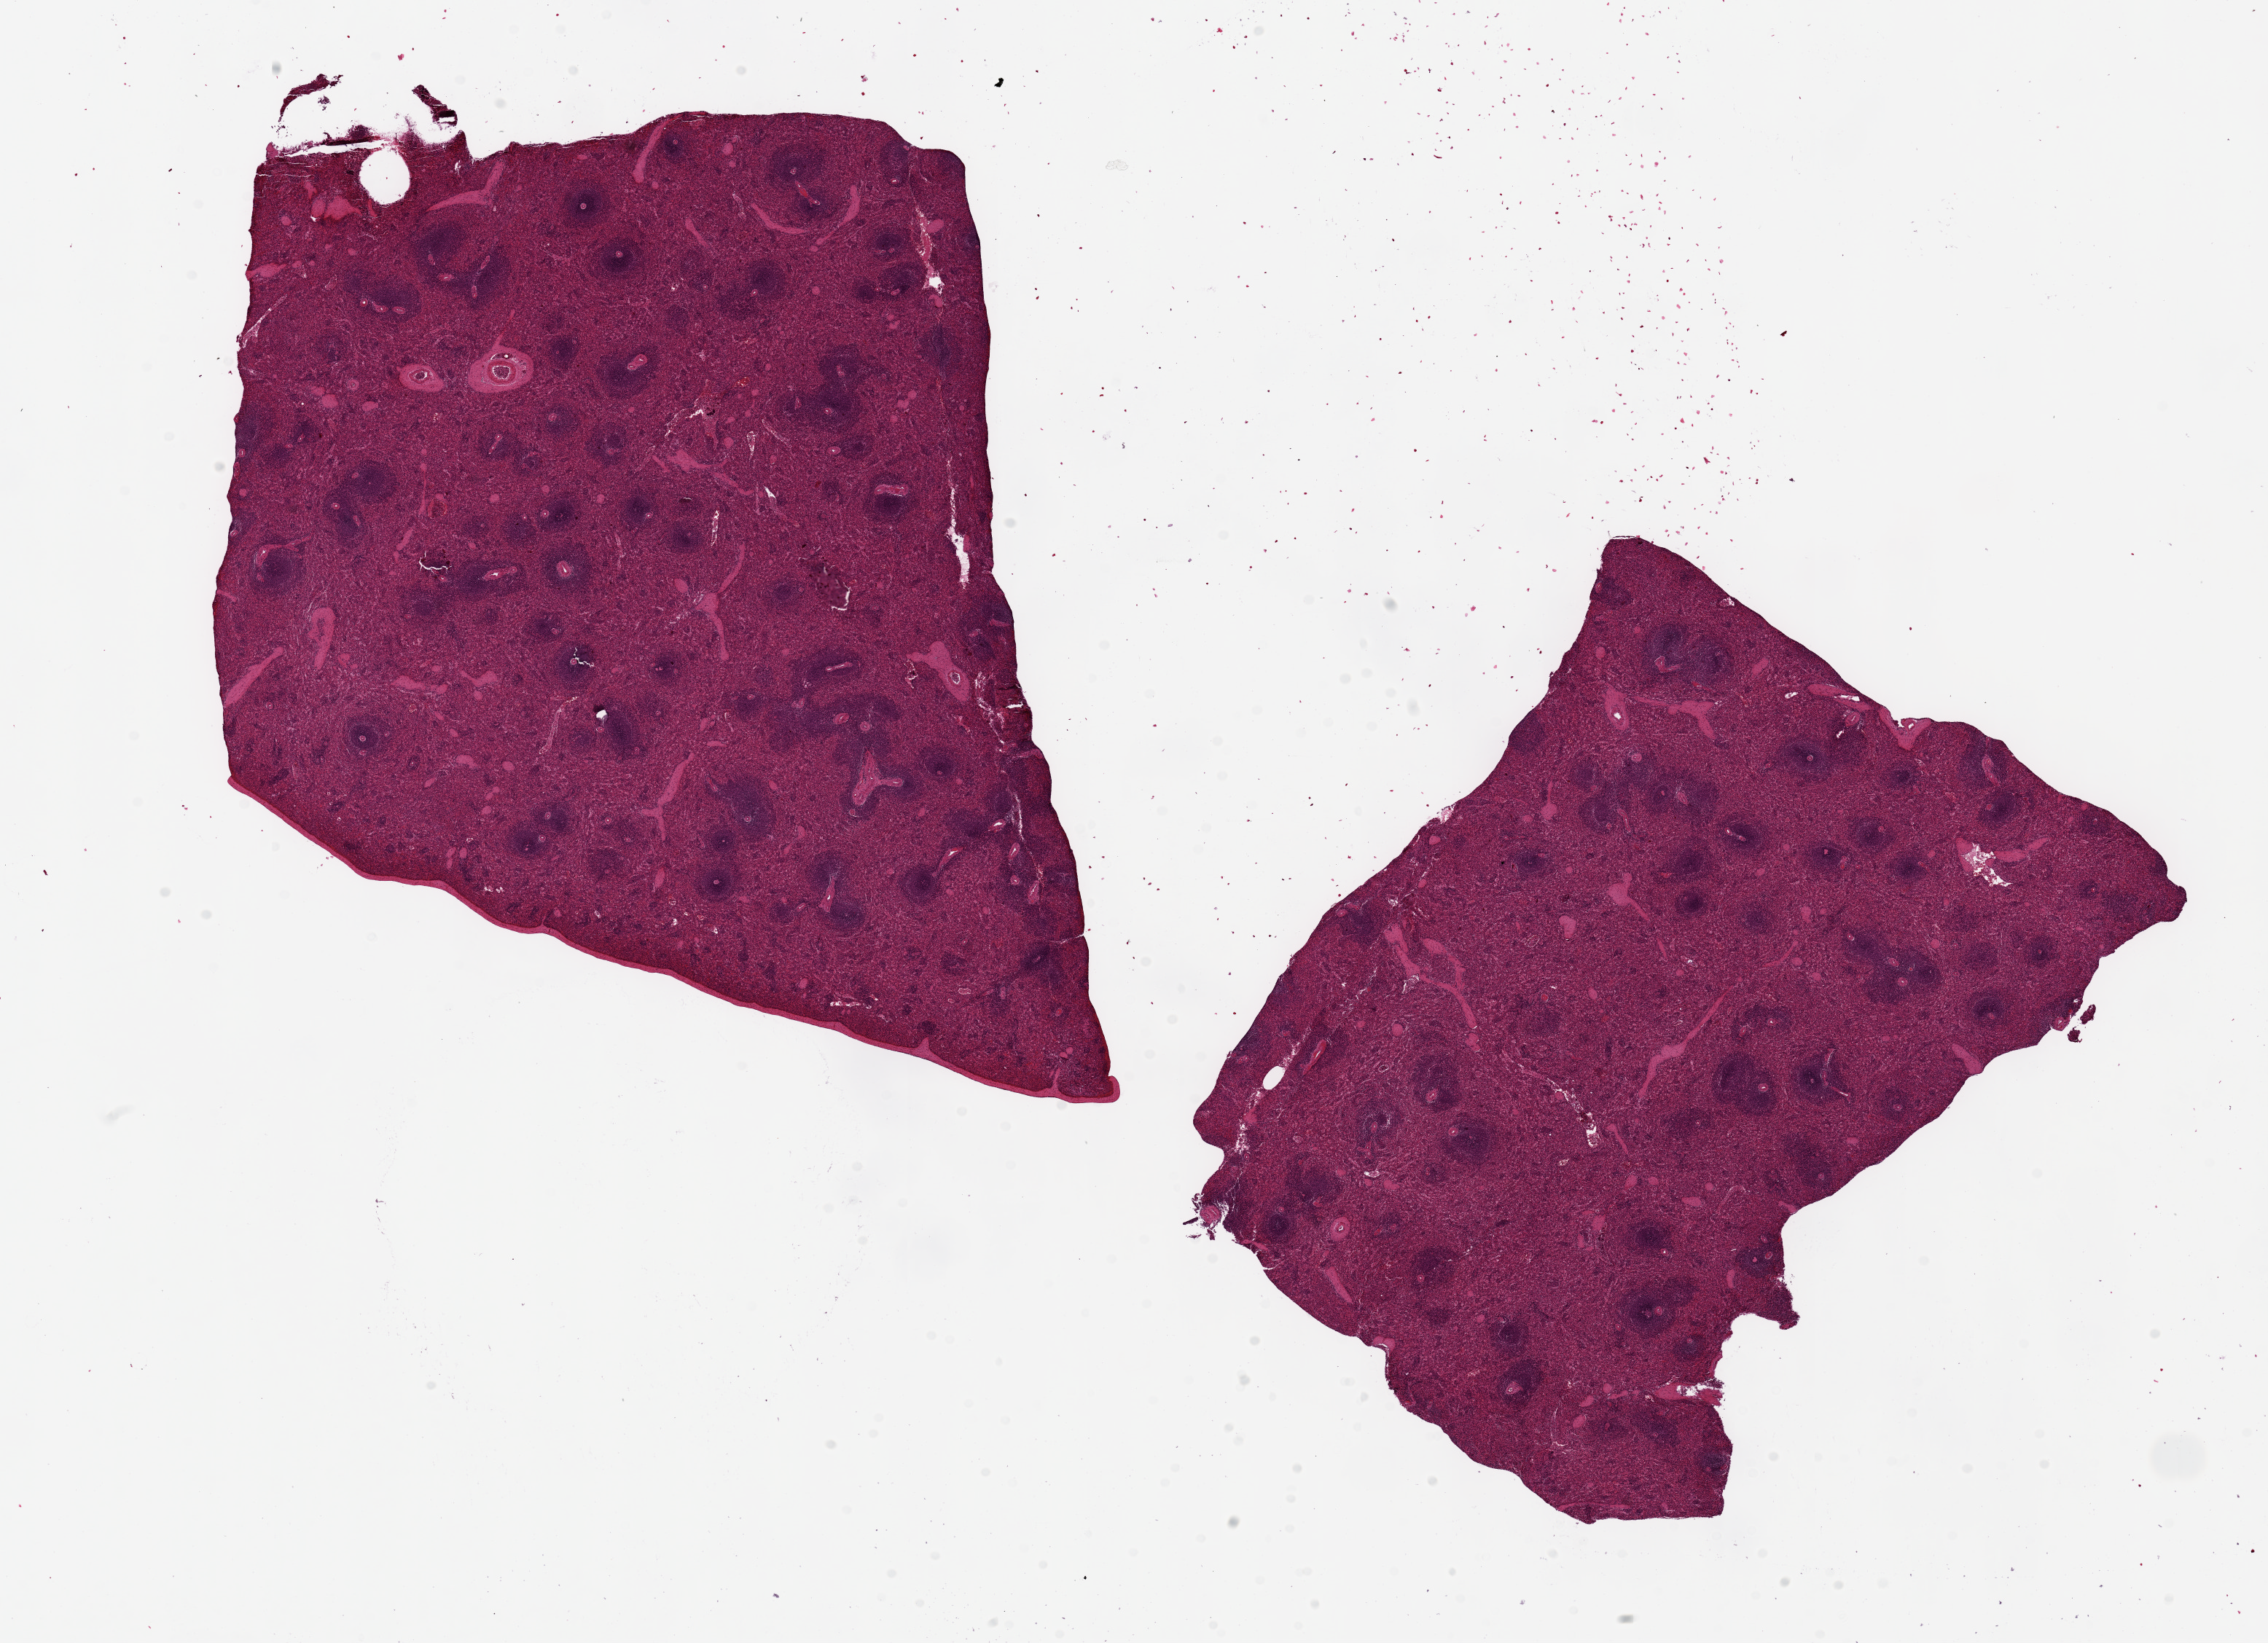
Digitized hematoxylin and eosin (H&E)-stained section — a low-resolution overview of the entire scanned area, about 24.6 x 17.8 mm; PAXgene-fixed, paraffin-embedded tissue; target tissue: spleen; donor tissue sample. Donor sex: male.
Review note (as recorded): 2 pieces ~10x7mm.